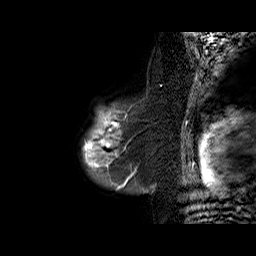
Breast MRI (dynamic contrast-enhanced), one sagittal slice; position 51 of 60 along the scan axis; dynamic contrast-enhanced series, time point 2 of 6 at this slice position (early post-contrast); 1.5 T; TE 6.3 ms, TR 32.4 ms; 256 × 256 image matrix. Female patient. Case-level facts recorded for this patient, not image findings: setting: breast cancer imaged before/during neoadjuvant chemotherapy; receptor status: triple-negative.
Annotated regions visible in this slice (semi-automatic segmentation, software-assisted and operator-edited):
- analysis volume of interest (the breast-tissue region the enhancement analysis was run in; not a lesion): bounding box <81,92,161,187> (left, top, right, bottom; pixels)
- tumour enhancement mask (voxels above the 100 % enhancement threshold inside the analysis volume of interest): <82,110,131,187>